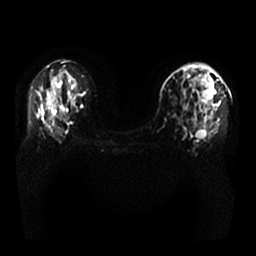
Breast MRI, one axial slice; diffusion-weighted series; image 2 of 4 stored at this slice position (different b-values; order by instance number); 1.5 T; 4 mm slice thickness; 256 × 256 image matrix, field of view 350 × 350 mm. Female patient.
Outlined on this slice (manually delineated by an expert):
- tumour on diffusion-weighted imaging: bounding box (x1, y1, x2, y2) in pixels: (202, 86, 214, 99)